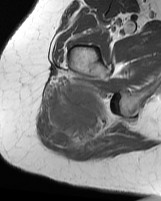
MRI of an extremity soft-tissue mass, one axial slice; slice 44 of 70 in the series (ordered by position); MR volume resampled by the dataset authors to the PET/CT grid (not the native acquisition matrix); 161 × 201 image matrix, field of view 157 × 196 mm. Female patient. From the clinical record (not read from this slice): histological type: synovial sarcoma; grade: intermediate; site of the primary tumour: right buttock.
Annotated regions visible in this slice (expert contour drawn on MRI and transferred to this co-registered scan by the dataset authors):
- gross tumour volume including surrounding oedema: bounding box (x1, y1, x2, y2) in pixels: (51, 81, 114, 153)
- gross tumour volume (mass): (51, 81, 105, 135)